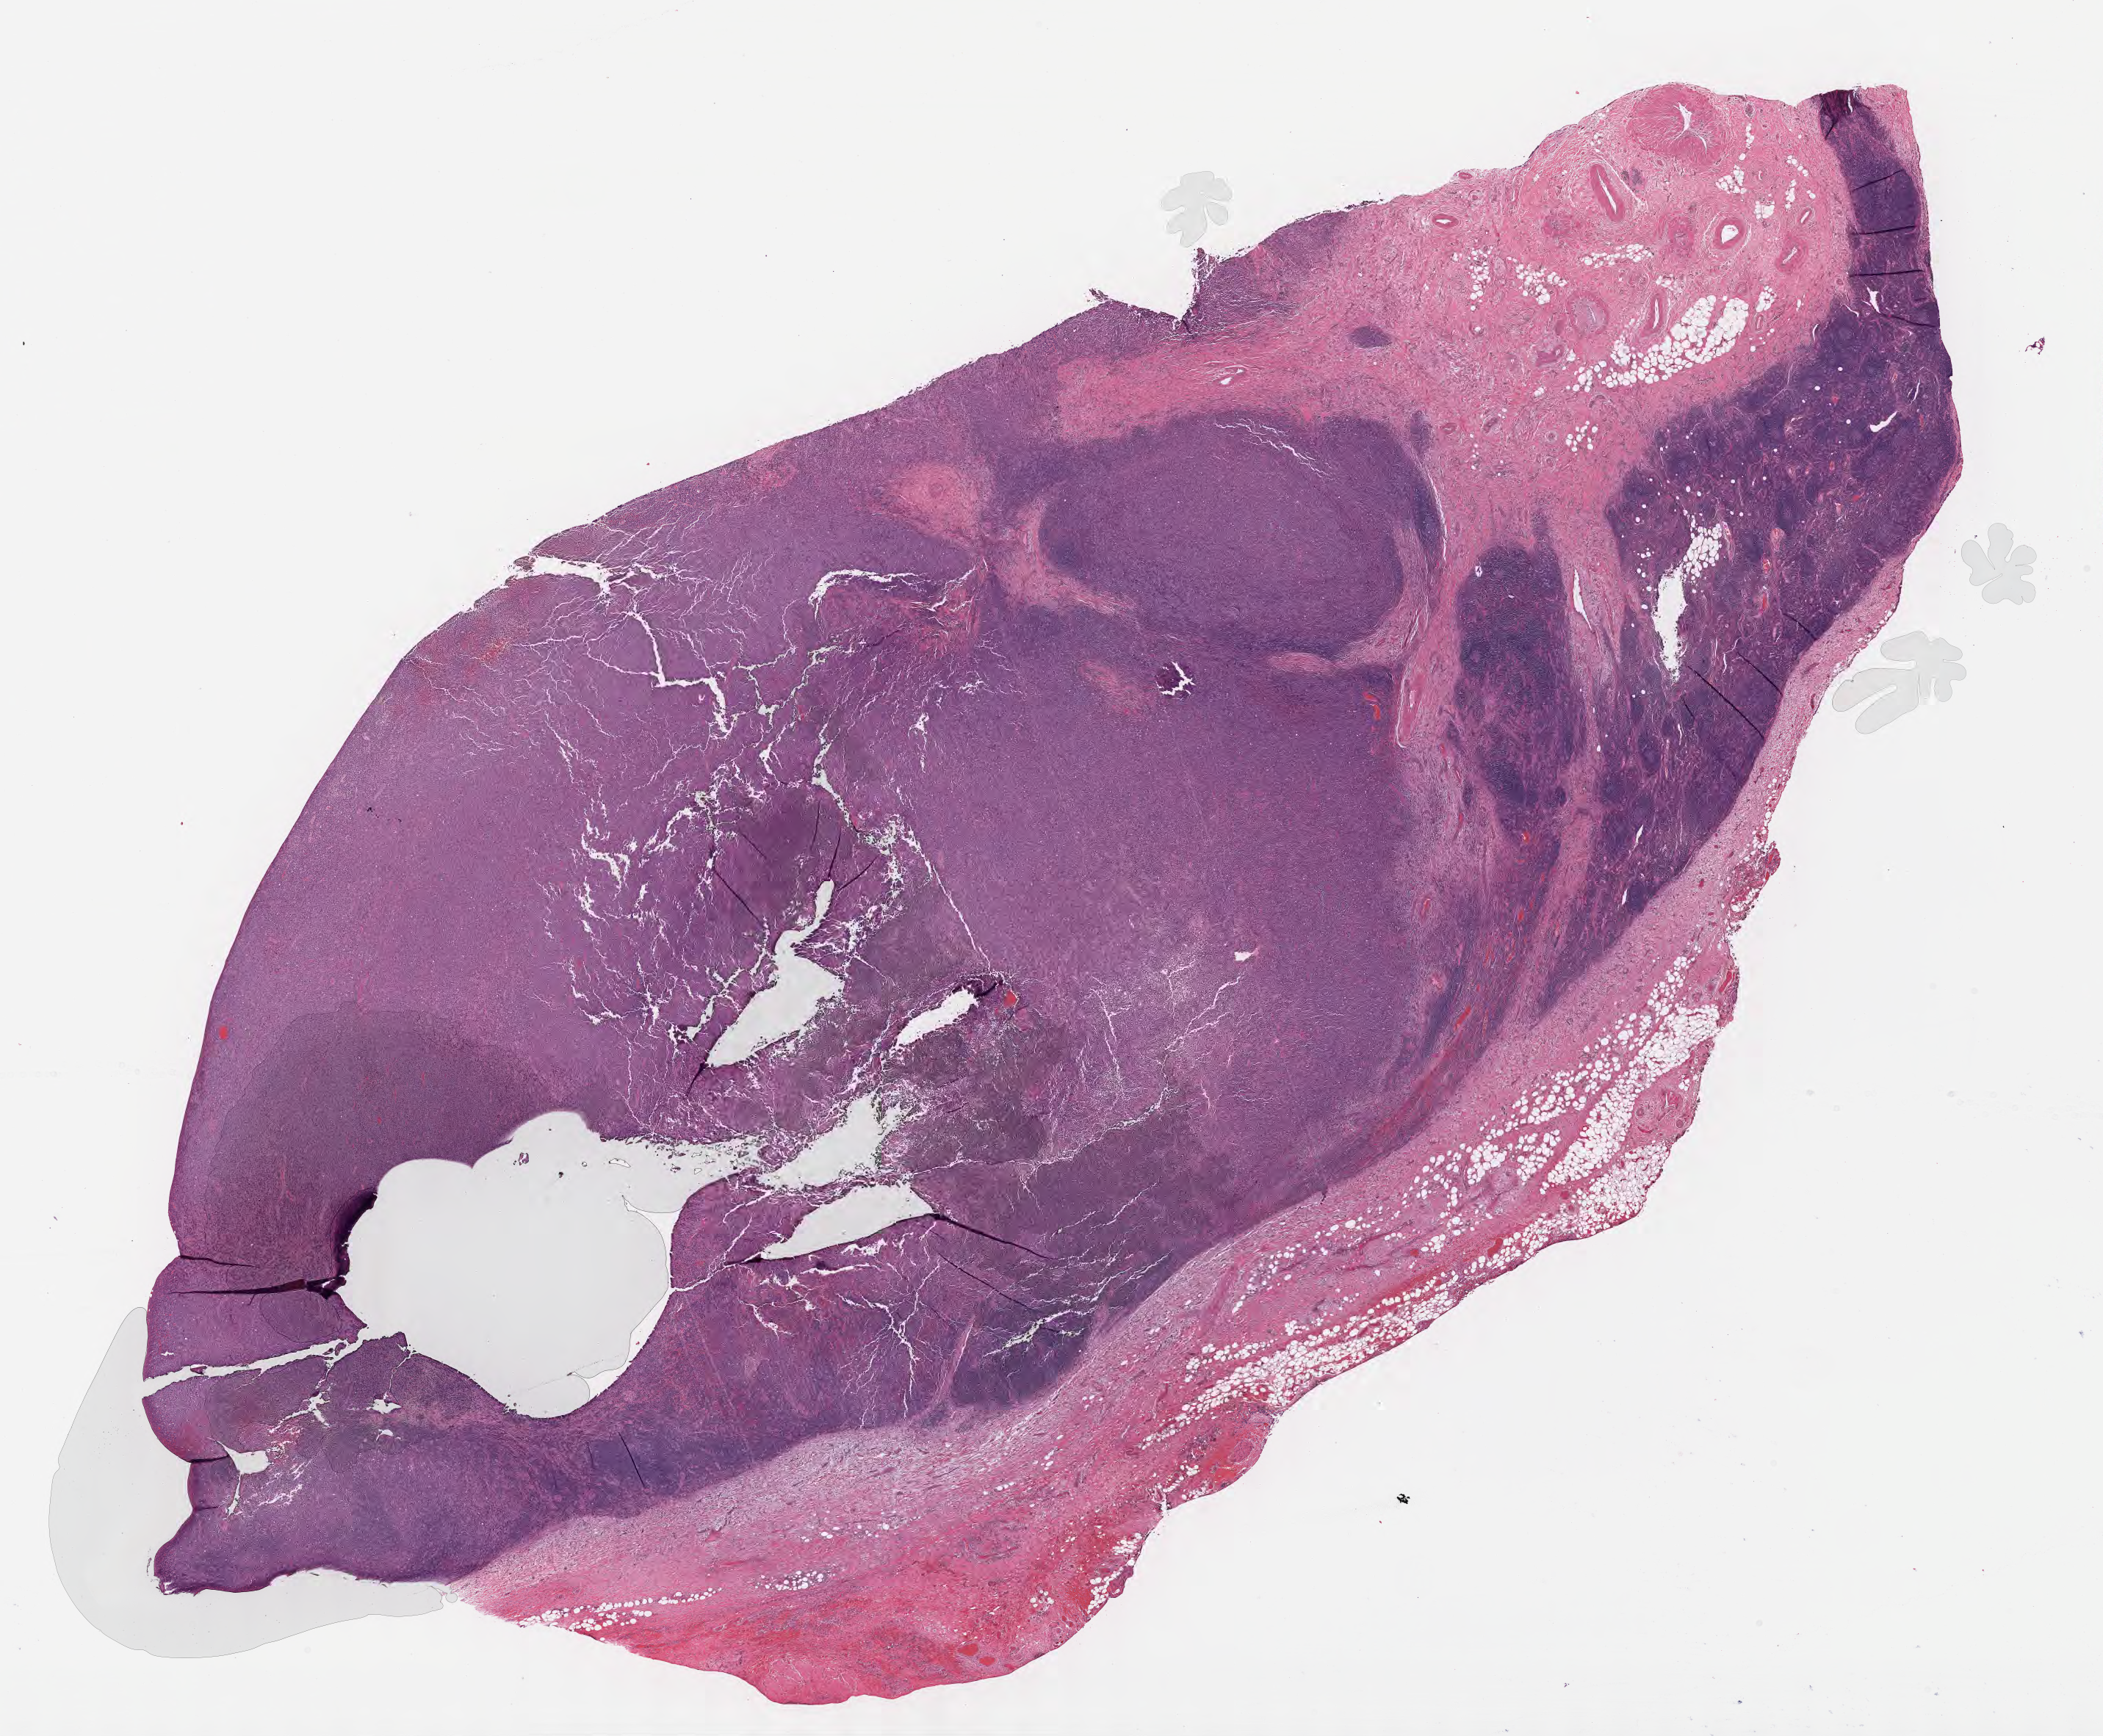
Digitized hematoxylin and eosin (H&E)-stained section — whole scanned area (about 23.1 x 19.1 mm) shown as a low-resolution overview; specimen: tumor tissue; site: lymph node. Patient: male, age 60 years.
Histologic diagnosis: Diffuse large B-cell lymphoma, NOS.